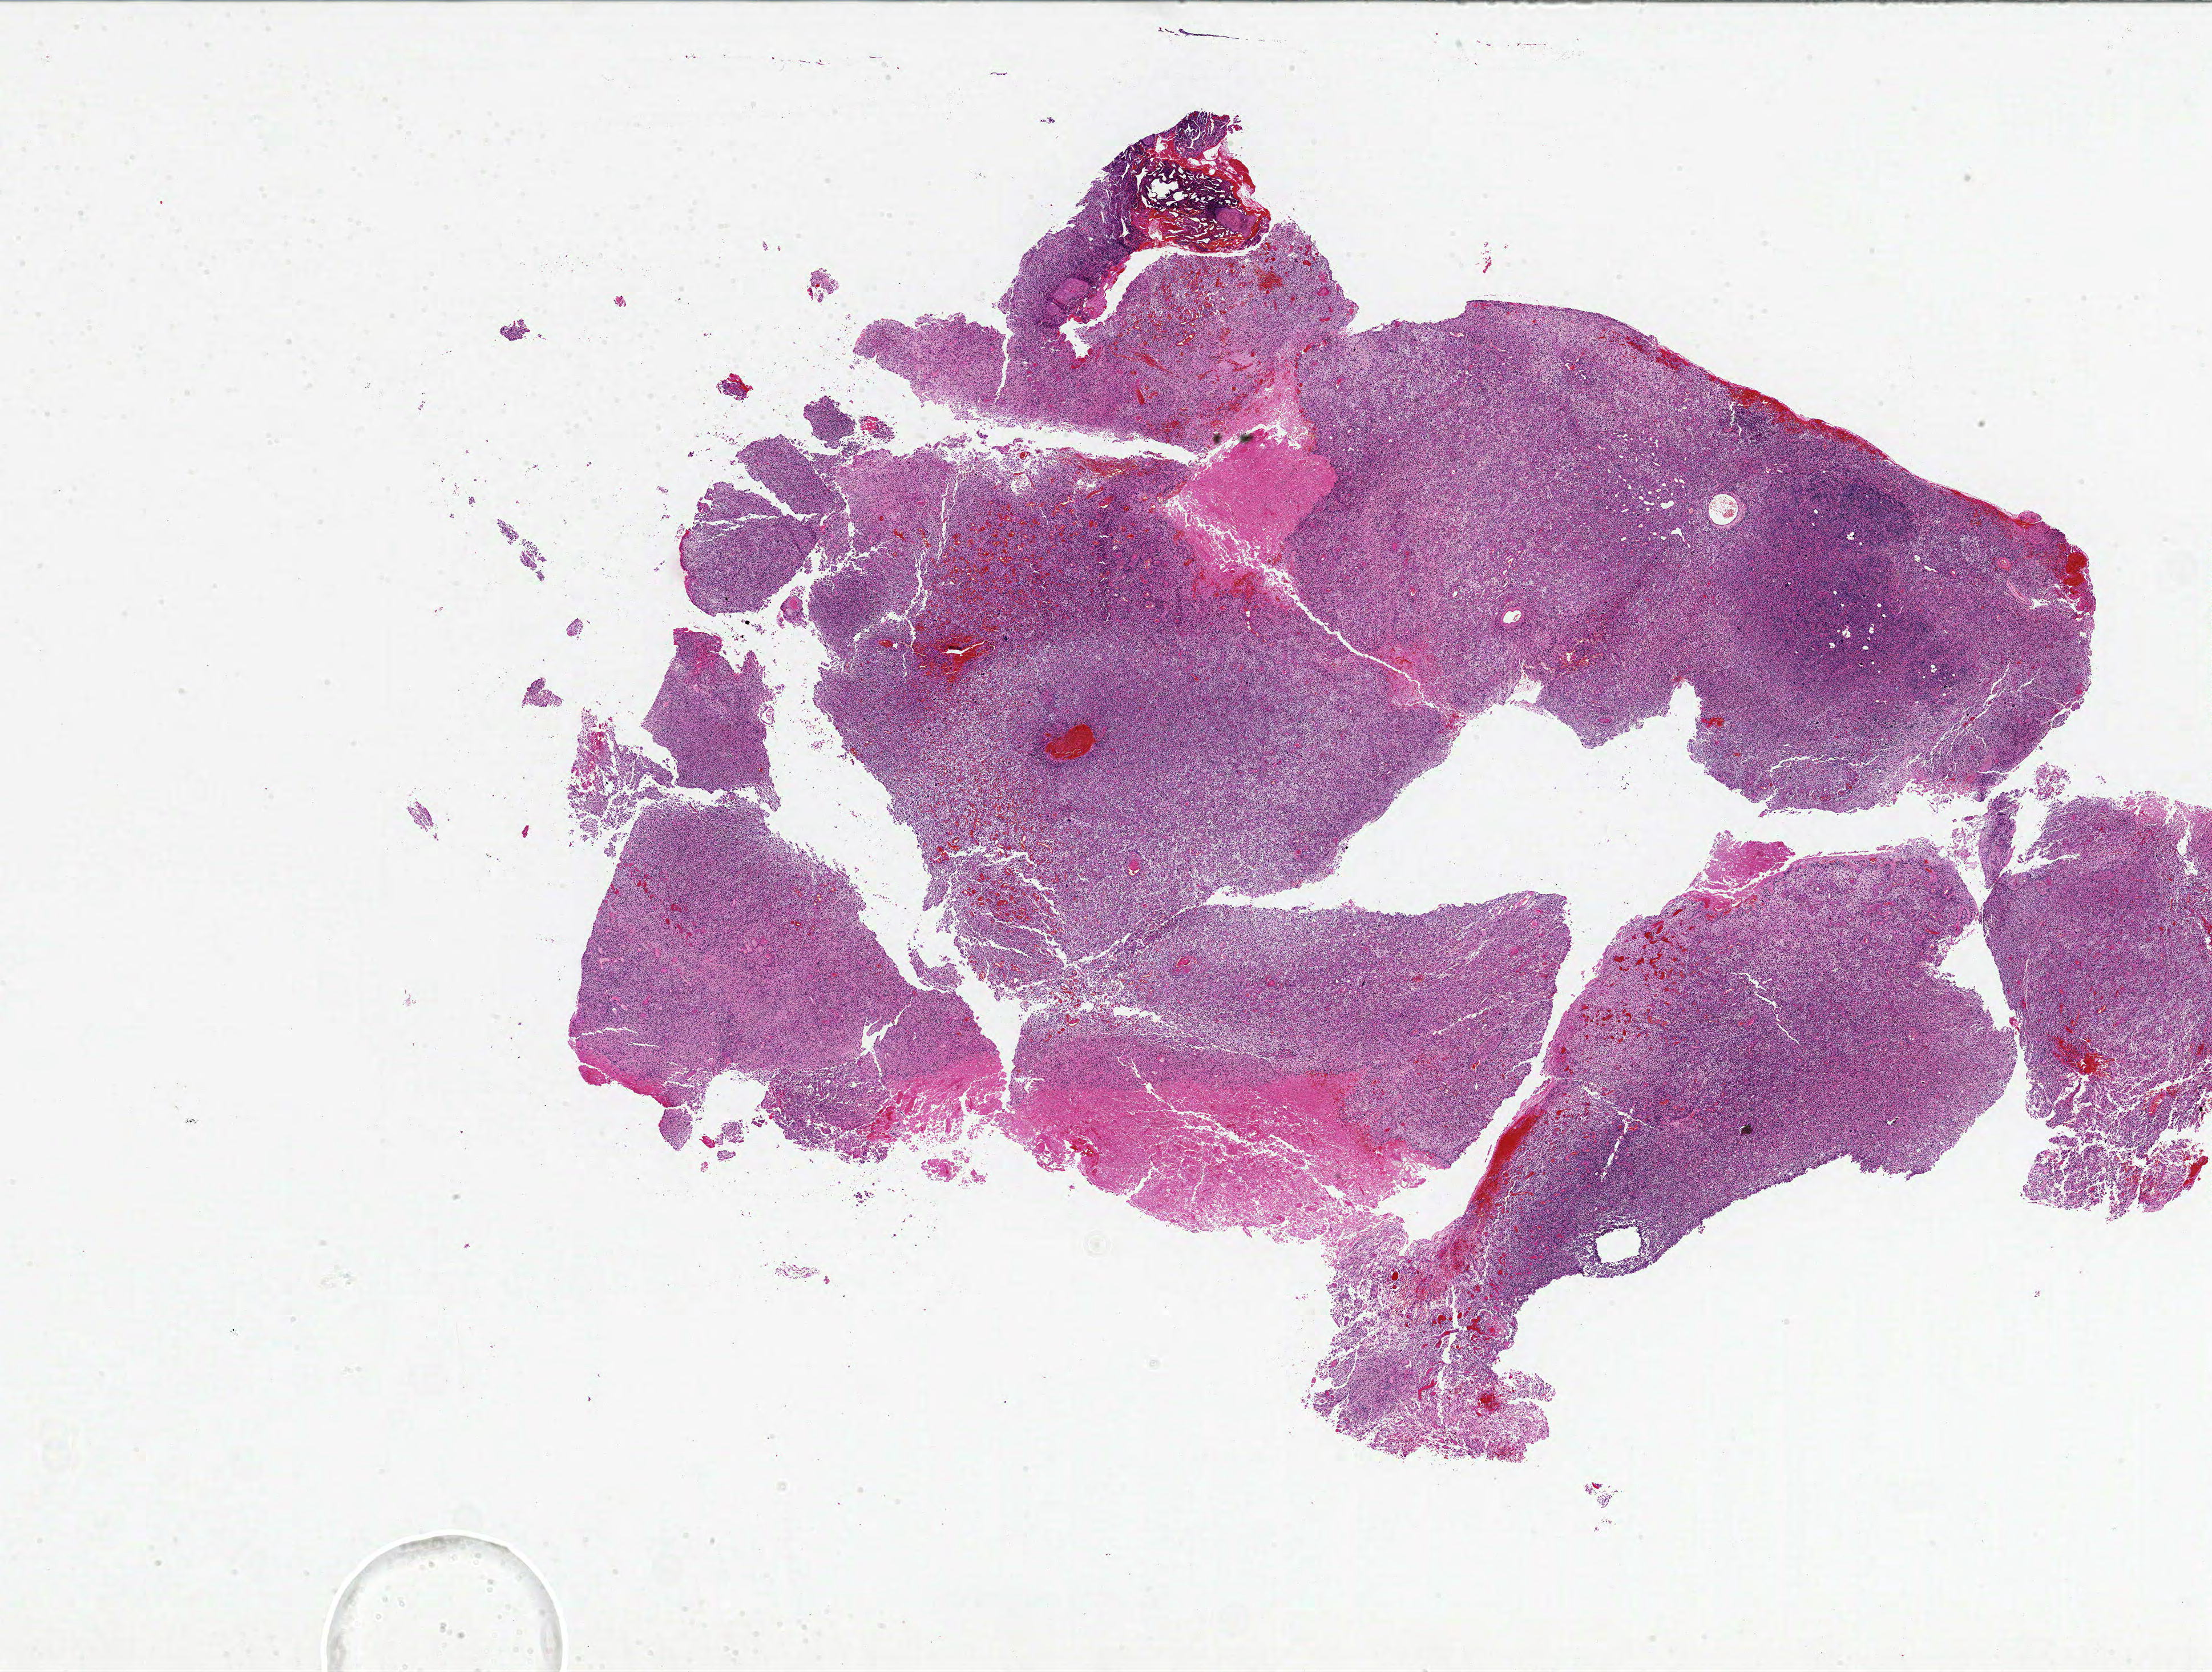
Digitized H&E-stained tissue section (whole slide) — whole scanned area (about 31.0 x 23.4 mm, acquisition: 20x scan) shown as a low-resolution overview, FFPE section, sample: primary tumour, brain. Male, age 86 years at initial diagnosis.
* diagnosis: Glioblastoma